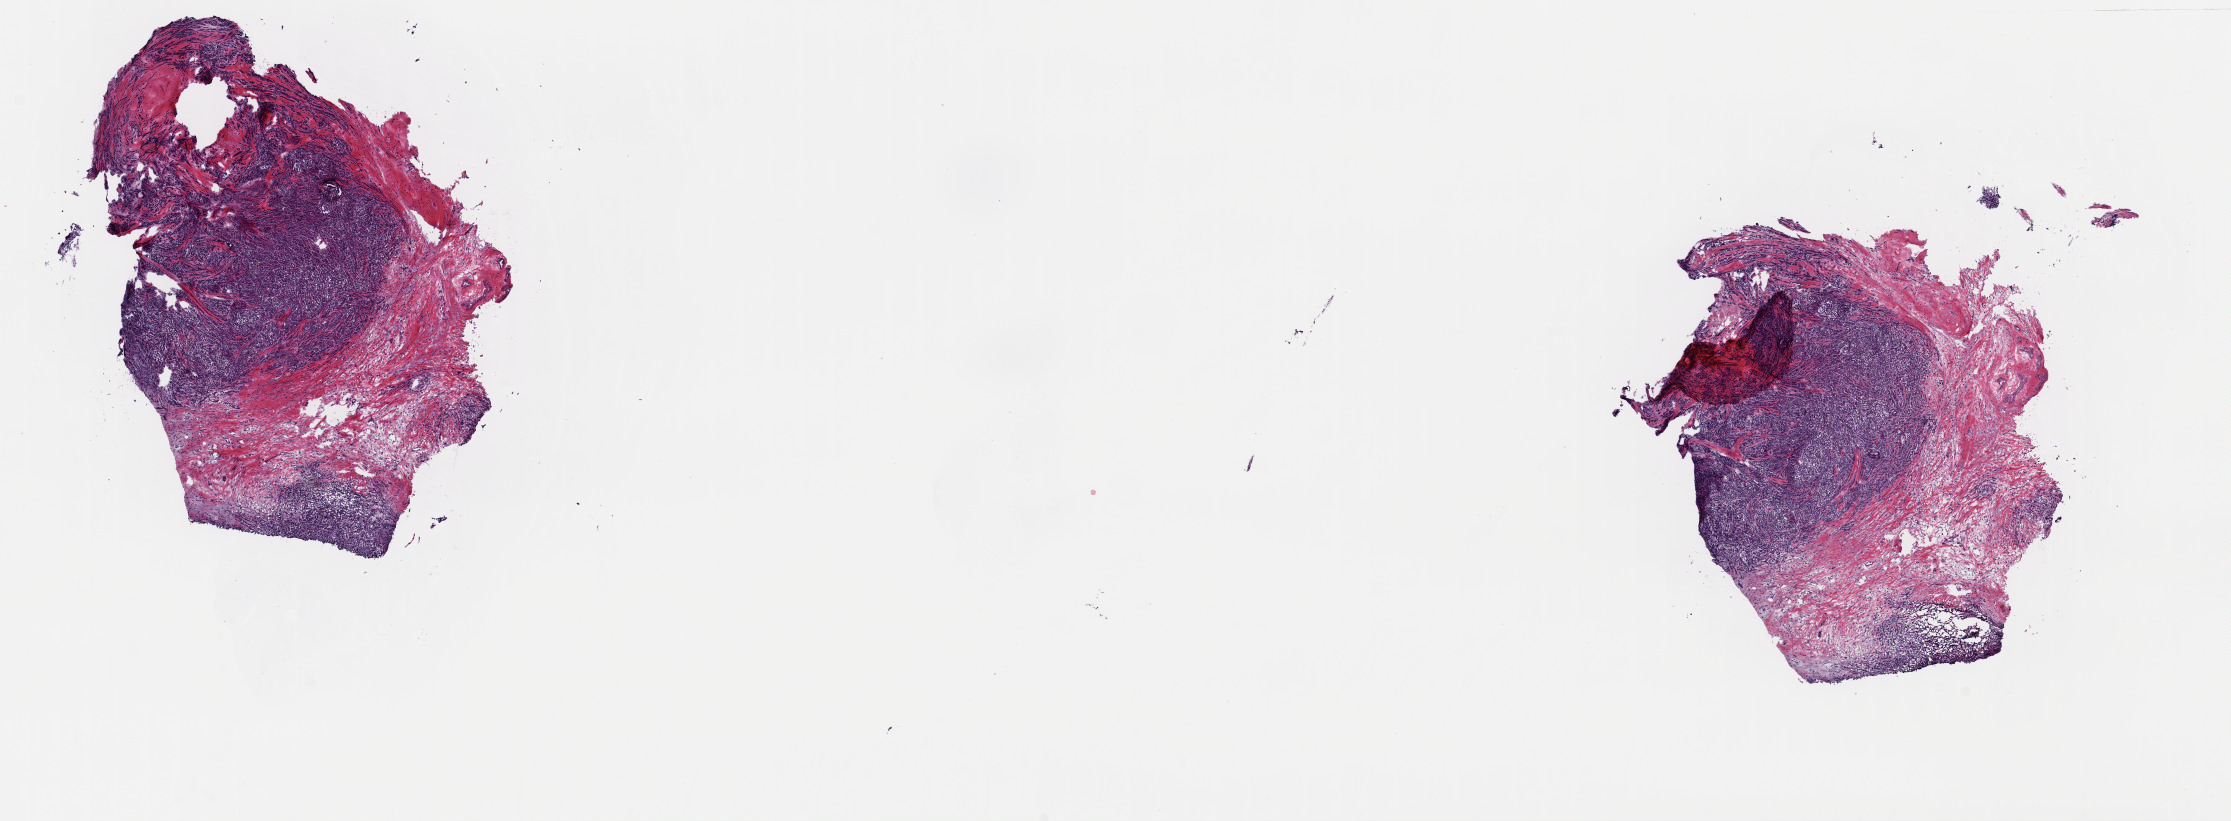
Whole-slide histology image, Hematoxylin and eosin (H&E) stained, low-resolution overview of the scanned area, about 17.6 x 6.5 mm (slide scanned at 40x), frozen section from the top of the tissue portion, breast, primary tumour sample. Patient: female, age at initial diagnosis 62 years. Pathologist review of this section (percent, as recorded): tumour cells 100%, tumour nuclei 88%, normal cells 0%, stromal cells 0%, necrosis 0%. Inflammatory infiltration, as recorded: lymphocyte infiltration 0%, monocyte infiltration 0%, neutrophil infiltration 0%.
AJCC pathologic stage: IIA (7th edition). Pathologic diagnosis: Lobular carcinoma, NOS.